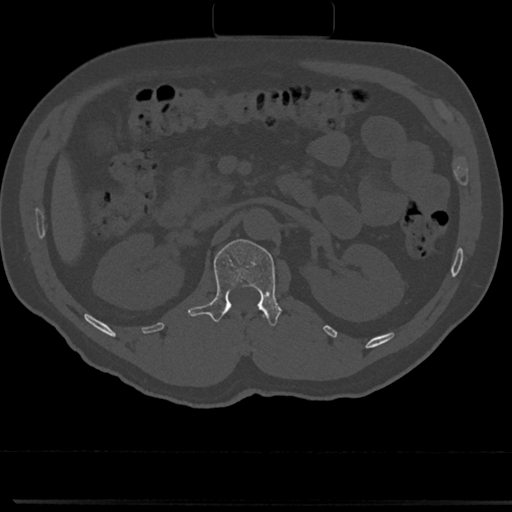
CT including the spine, one axial slice; slice 91 of 817 in the series (ordered by position); reconstruction kernel Br40s/3; 120 kVp; bone window (W 1800 / L 400 HU); 0.5 mm slice thickness; 512 × 512 image matrix, field of view 355 × 355 mm. Male patient, age 61 years. Case-level facts recorded for this patient, not image findings: primary cancer: prostate.
Structures marked on this image (semi-automatically segmented with operator editing):
- L1 vertebra: bounding box [x1, y1, x2, y2] px = [191, 239, 282, 326]